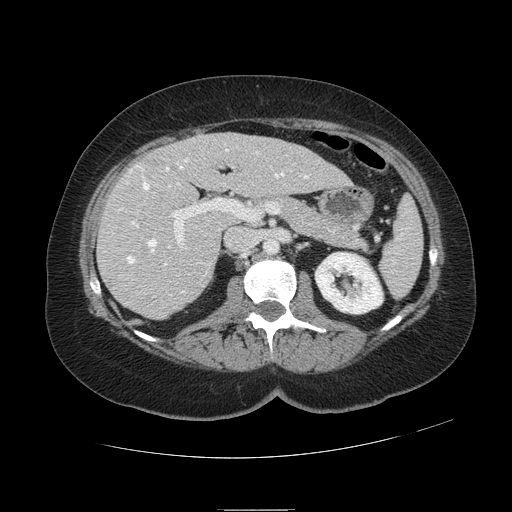
Contrast-enhanced abdominal CT, one axial slice. Slice 53 of 121 in the series (ordered by position). 120 kVp. Intravenous contrast given. Soft-tissue window (W 400 / L 40 HU). 2.5 mm slice thickness. 512 × 512 image matrix, field of view 400 × 400 mm. Female patient, age 52 years. Case-level facts recorded for this patient, not image findings: diagnosis: colorectal cancer liver metastases, imaged before liver resection; multiple liver metastases: yes; largest metastasis: 6.3 cm; disease in both lobes: no.
Outlined on this slice (outlined manually by an expert reader):
- hepatic veins: box from (x=120, y=150) to (x=308, y=293) px
- liver: (x=99, y=134)–(x=348, y=318)
- planned liver remnant (the part of the liver to remain after resection): (x=170, y=134)–(x=348, y=197)
- portal vein (with intrahepatic branches): (x=131, y=170)–(x=291, y=266)